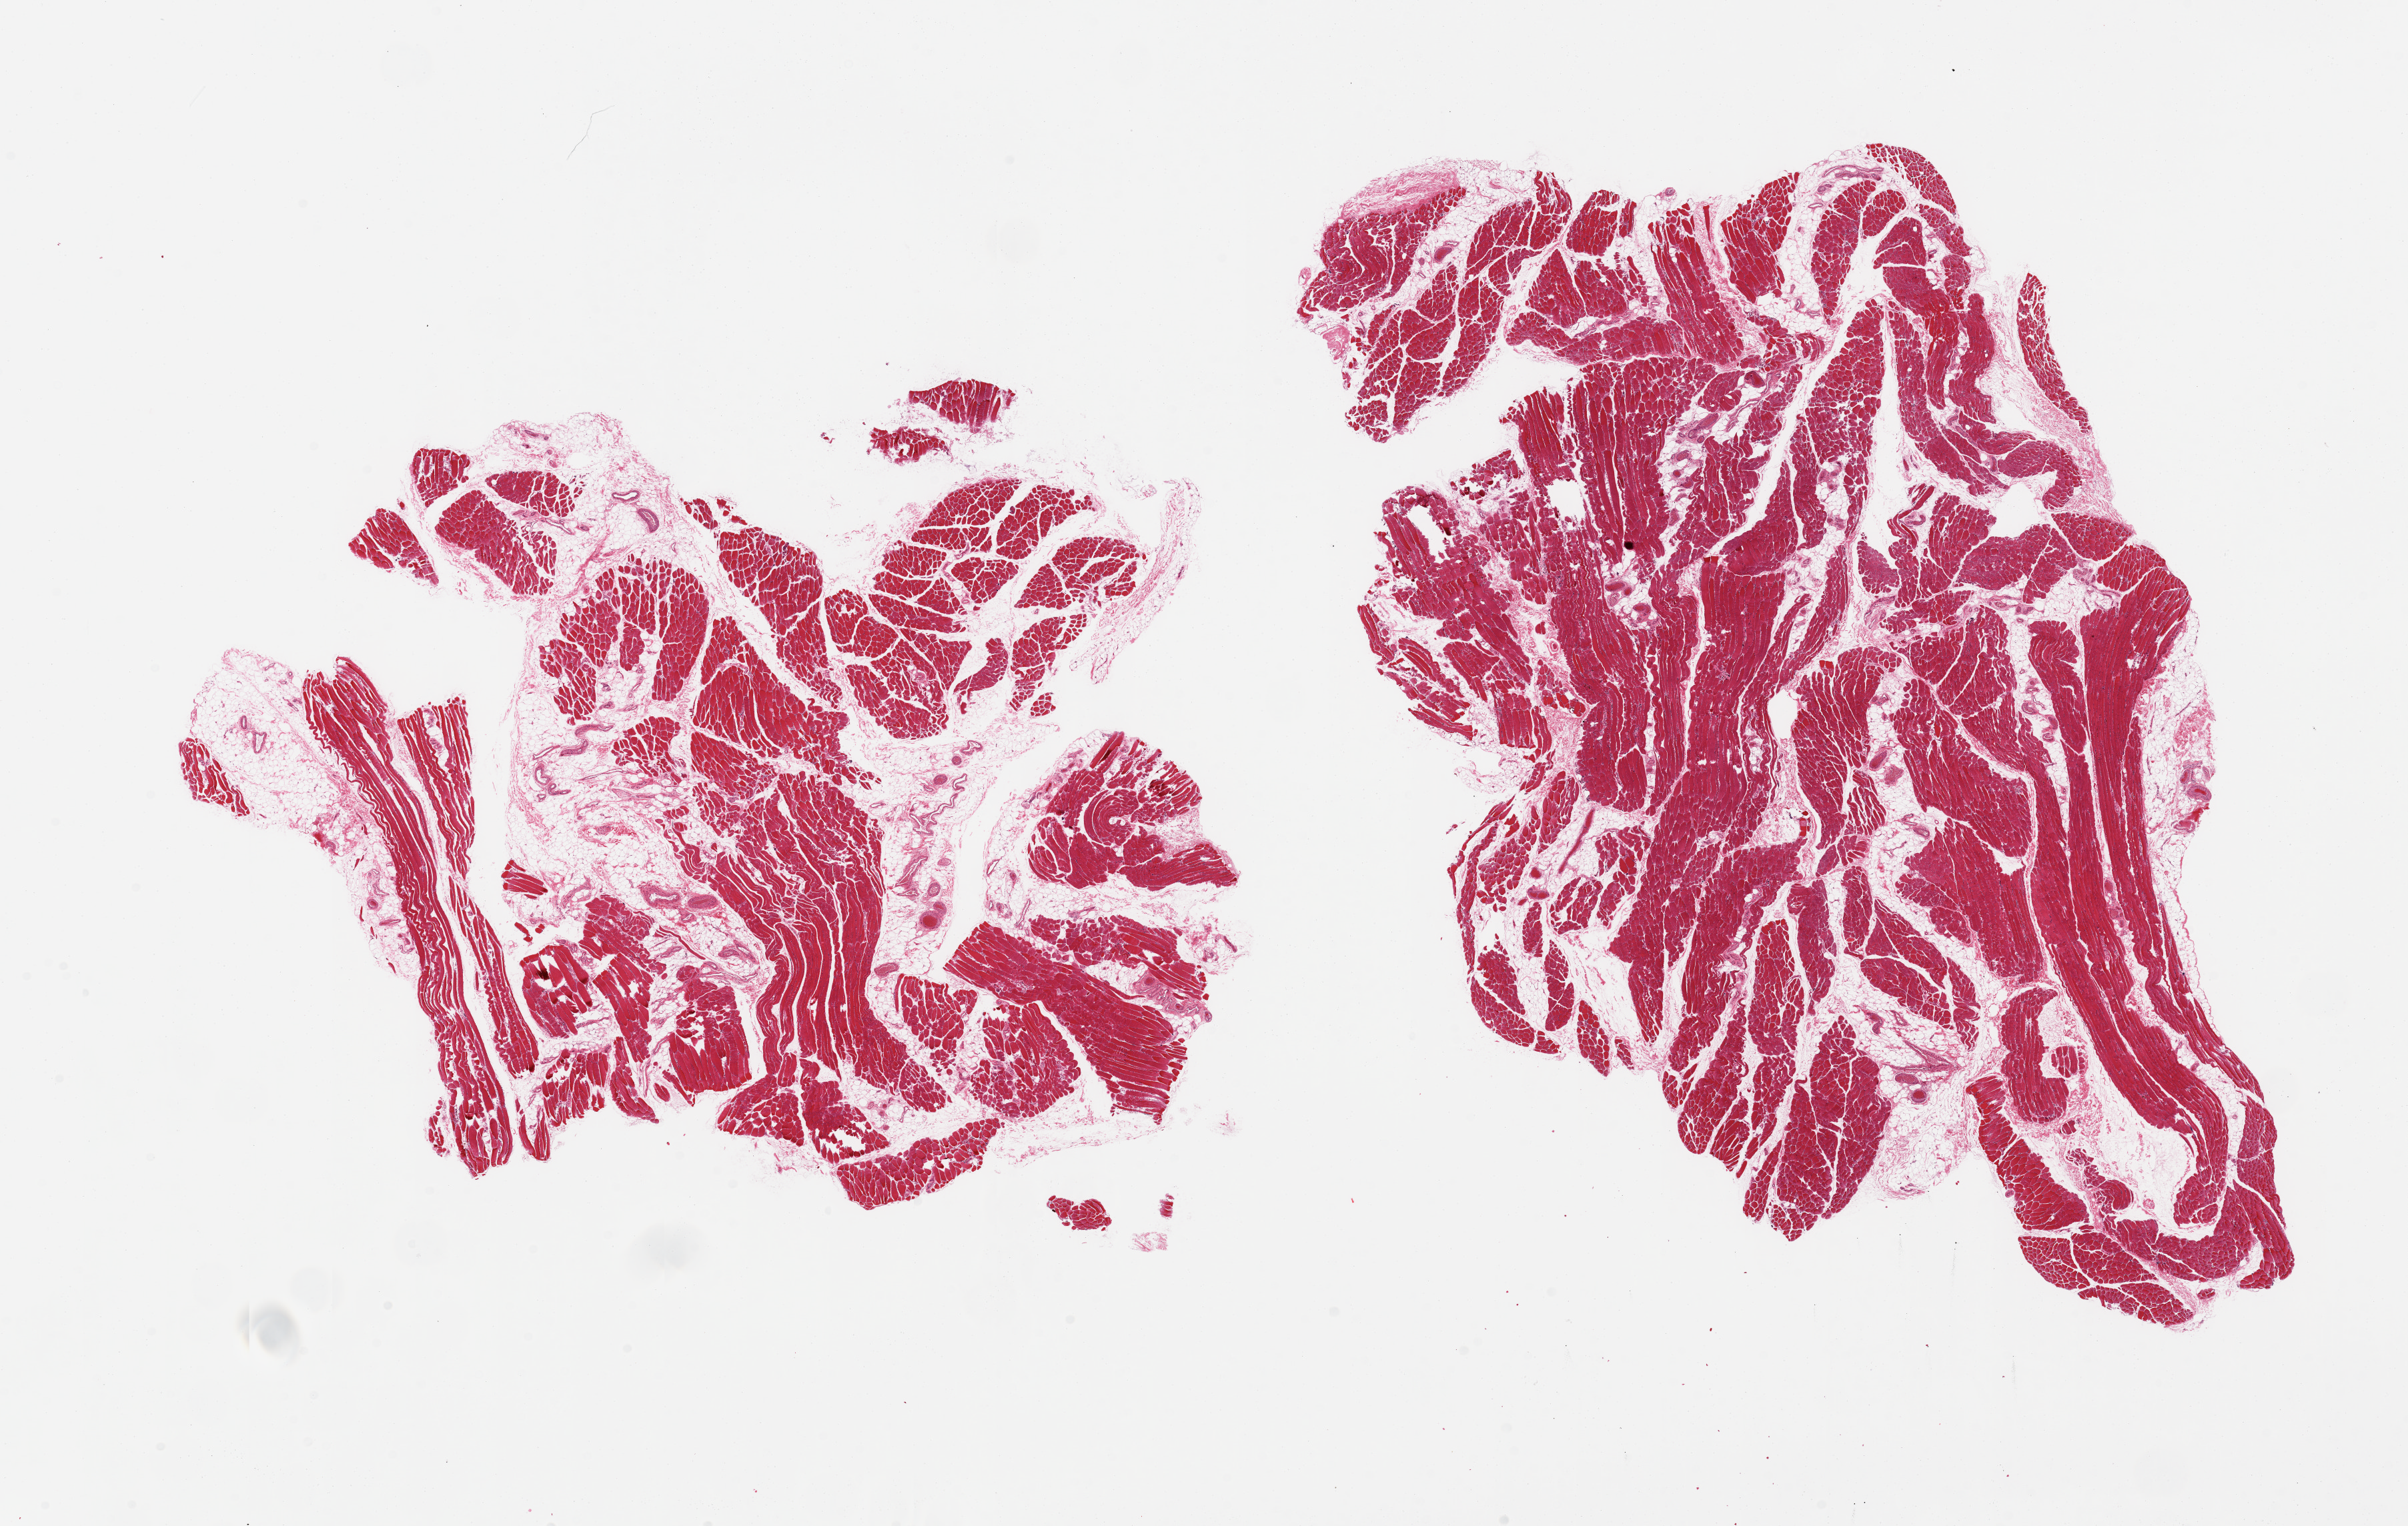
Digitized hematoxylin and eosin (H&E)-stained section, shown as a low-resolution overview of the whole scanned area (about 28.5 x 18.1 mm). PAXgene-fixed, paraffin-embedded tissue. Sampled site (target tissue): skeletal muscle. Donor tissue sample. Male donor.
• pathologist's review note for this sample: 2 pieces; up to 20% internal fat